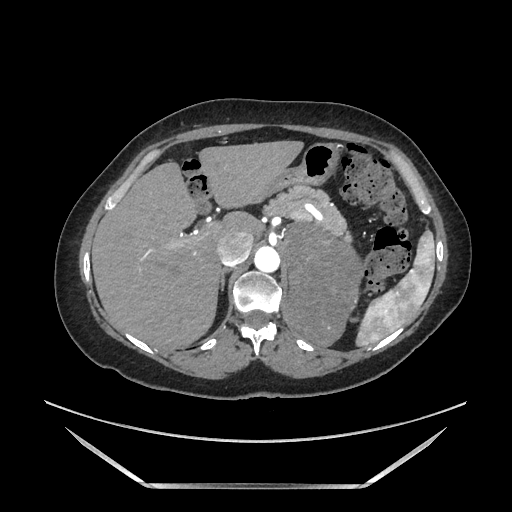
Contrast-enhanced abdominal CT, one axial slice; slice 124 of 205 in the series (ordered by position); soft-tissue window (W 400 / L 40 HU); 512 × 512 image matrix. Female patient. From the clinical record (not read from this slice): diagnosis: adrenocortical carcinoma; tumour side: left adrenal; tumour size at pathology: 12.5 cm; Ki-67 index: 39 %; stage (as recorded): 3.
Annotated regions visible in this slice (semi-automatically segmented with operator editing):
- mass: bounding box [x1, y1, x2, y2] px = [289, 226, 363, 343]